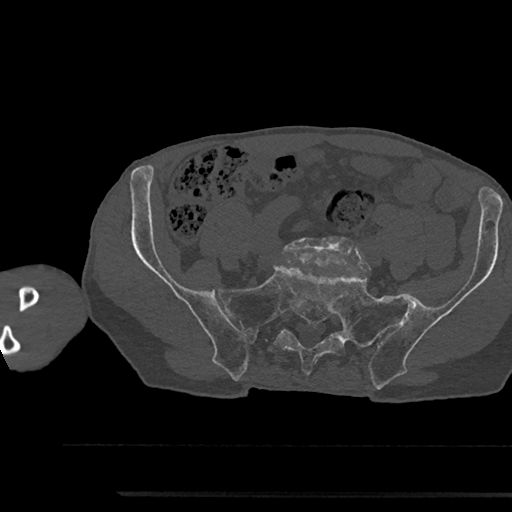
CT including the spine, one axial slice; position 291 of 797 along the scan axis; 120 kVp; bone window (W 1800 / L 400 HU); 0.5 mm slice thickness; 512 × 512 image matrix, field of view 367 × 367 mm. Male patient, age 79 years. Case-level facts recorded for this patient, not image findings: primary cancer: prostate.
Outlined on this slice (semi-automatically segmented with operator editing):
- L5 vertebra: bounding box (x1, y1, x2, y2) in pixels: (283, 237, 359, 268)